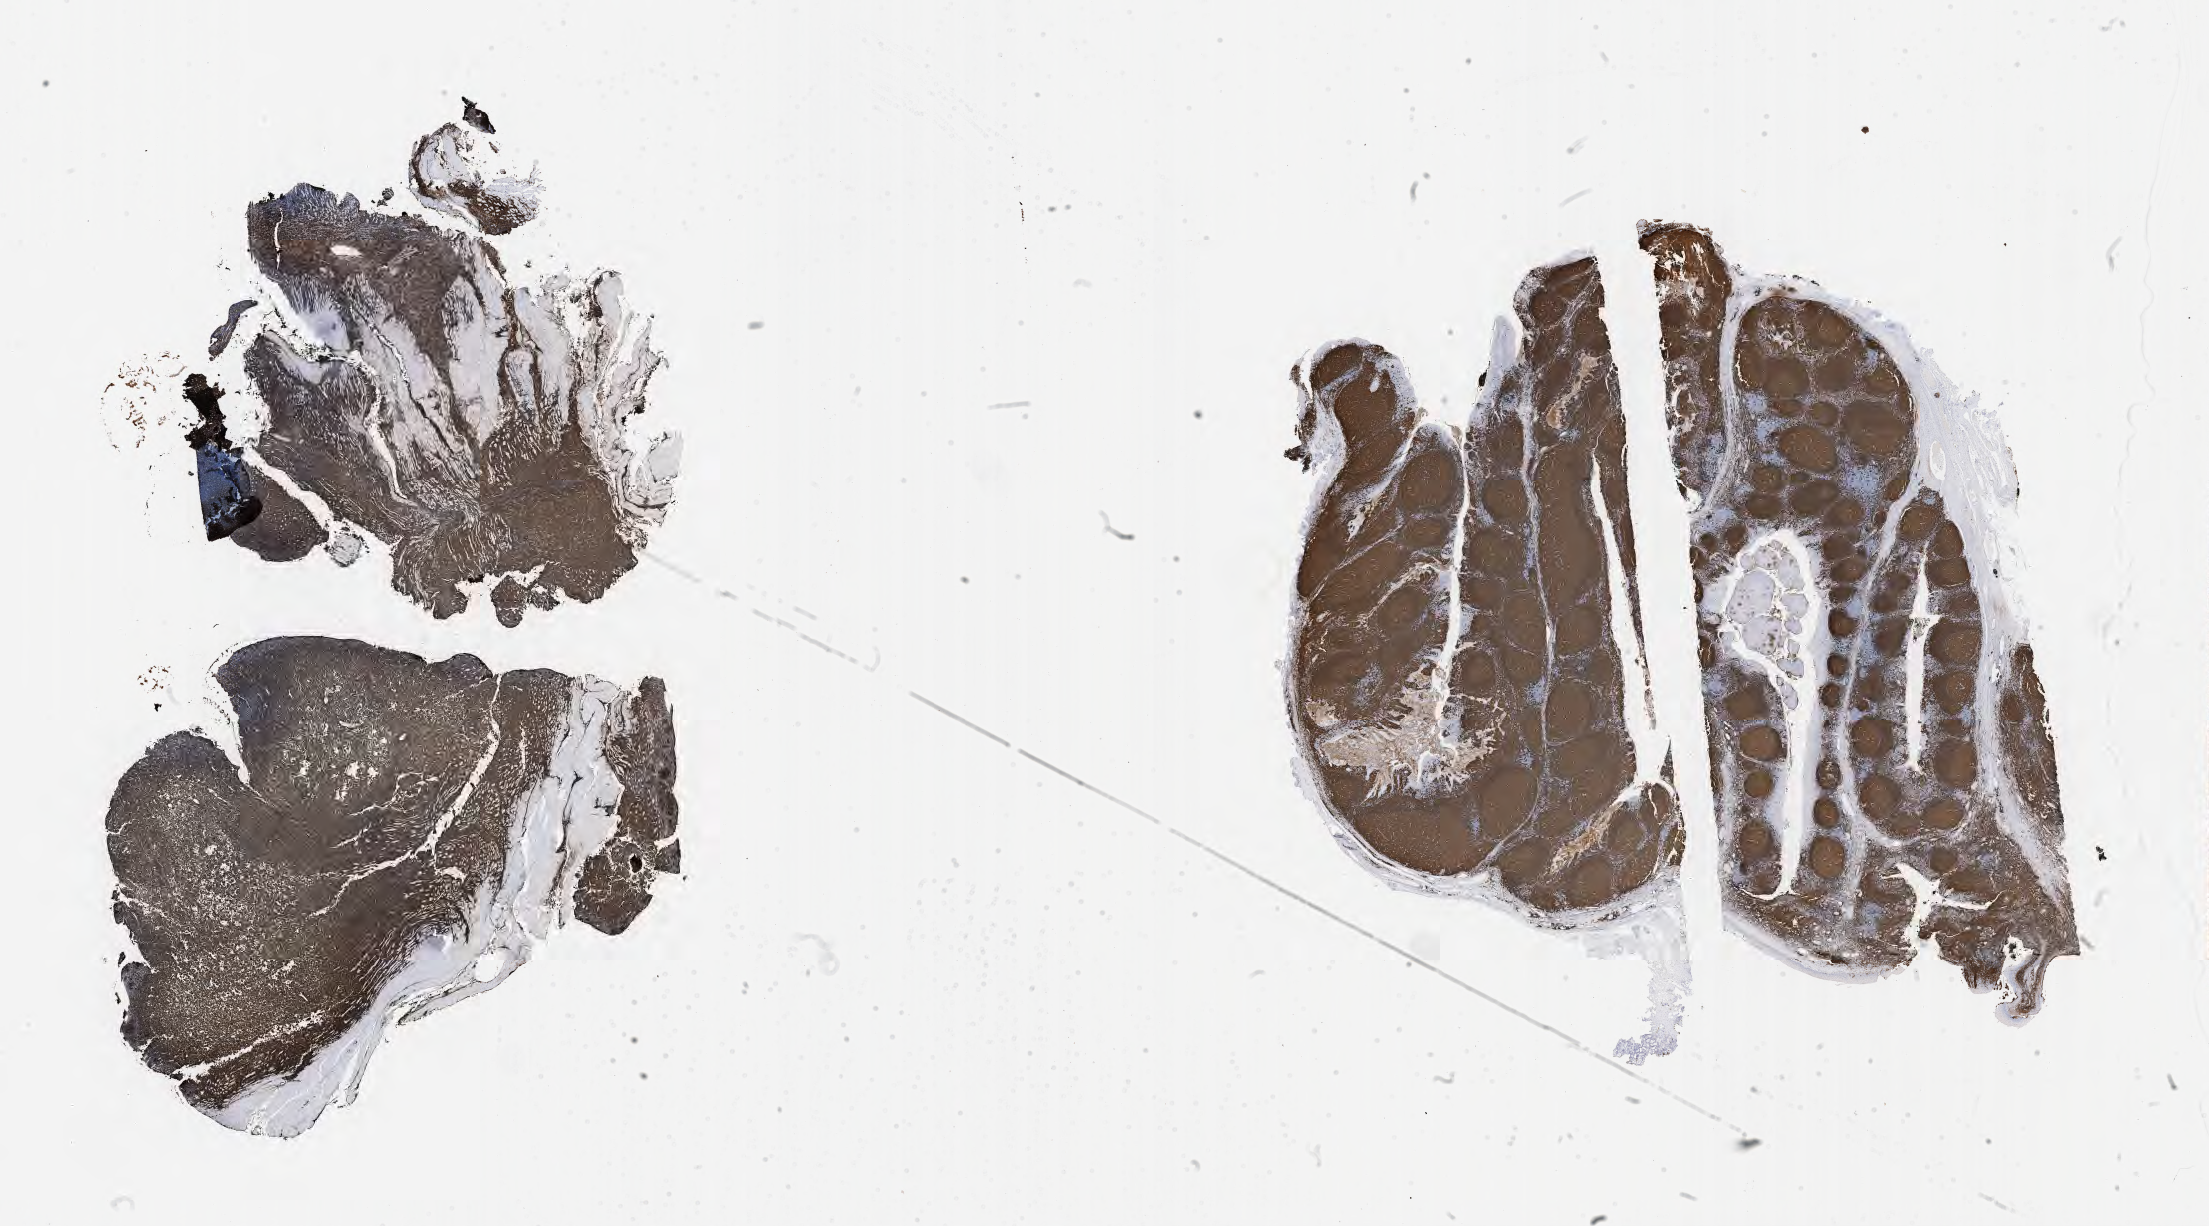
Immunohistochemistry (IHC) whole-slide image stained for CD20 — shown as a low-resolution overview of the whole scanned area (about 35.7 x 19.8 mm). Specimen: tumor tissue. Patient male; 40 years old.
Diagnosis: Burkitt lymphoma, NOS.